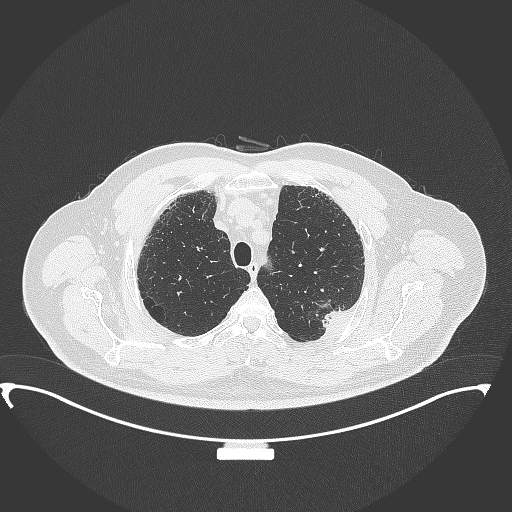
Chest CT, one axial slice; position 295 of 350 along the scan axis; reconstruction kernel B70f; 120 kVp; lung window (W 1500 / L -600 HU); 1 mm slice thickness; 512 × 512 image matrix, field of view 459 × 459 mm. Patient: male, 64 years. From the clinical record (not read from this slice): clinical TNM (as recorded): T1c N1 M1.
Annotated regions visible in this slice (bounding box drawn by a radiologist):
- lung tumour (recorded histology: adenocarcinoma): box from (x=314, y=300) to (x=353, y=337) px